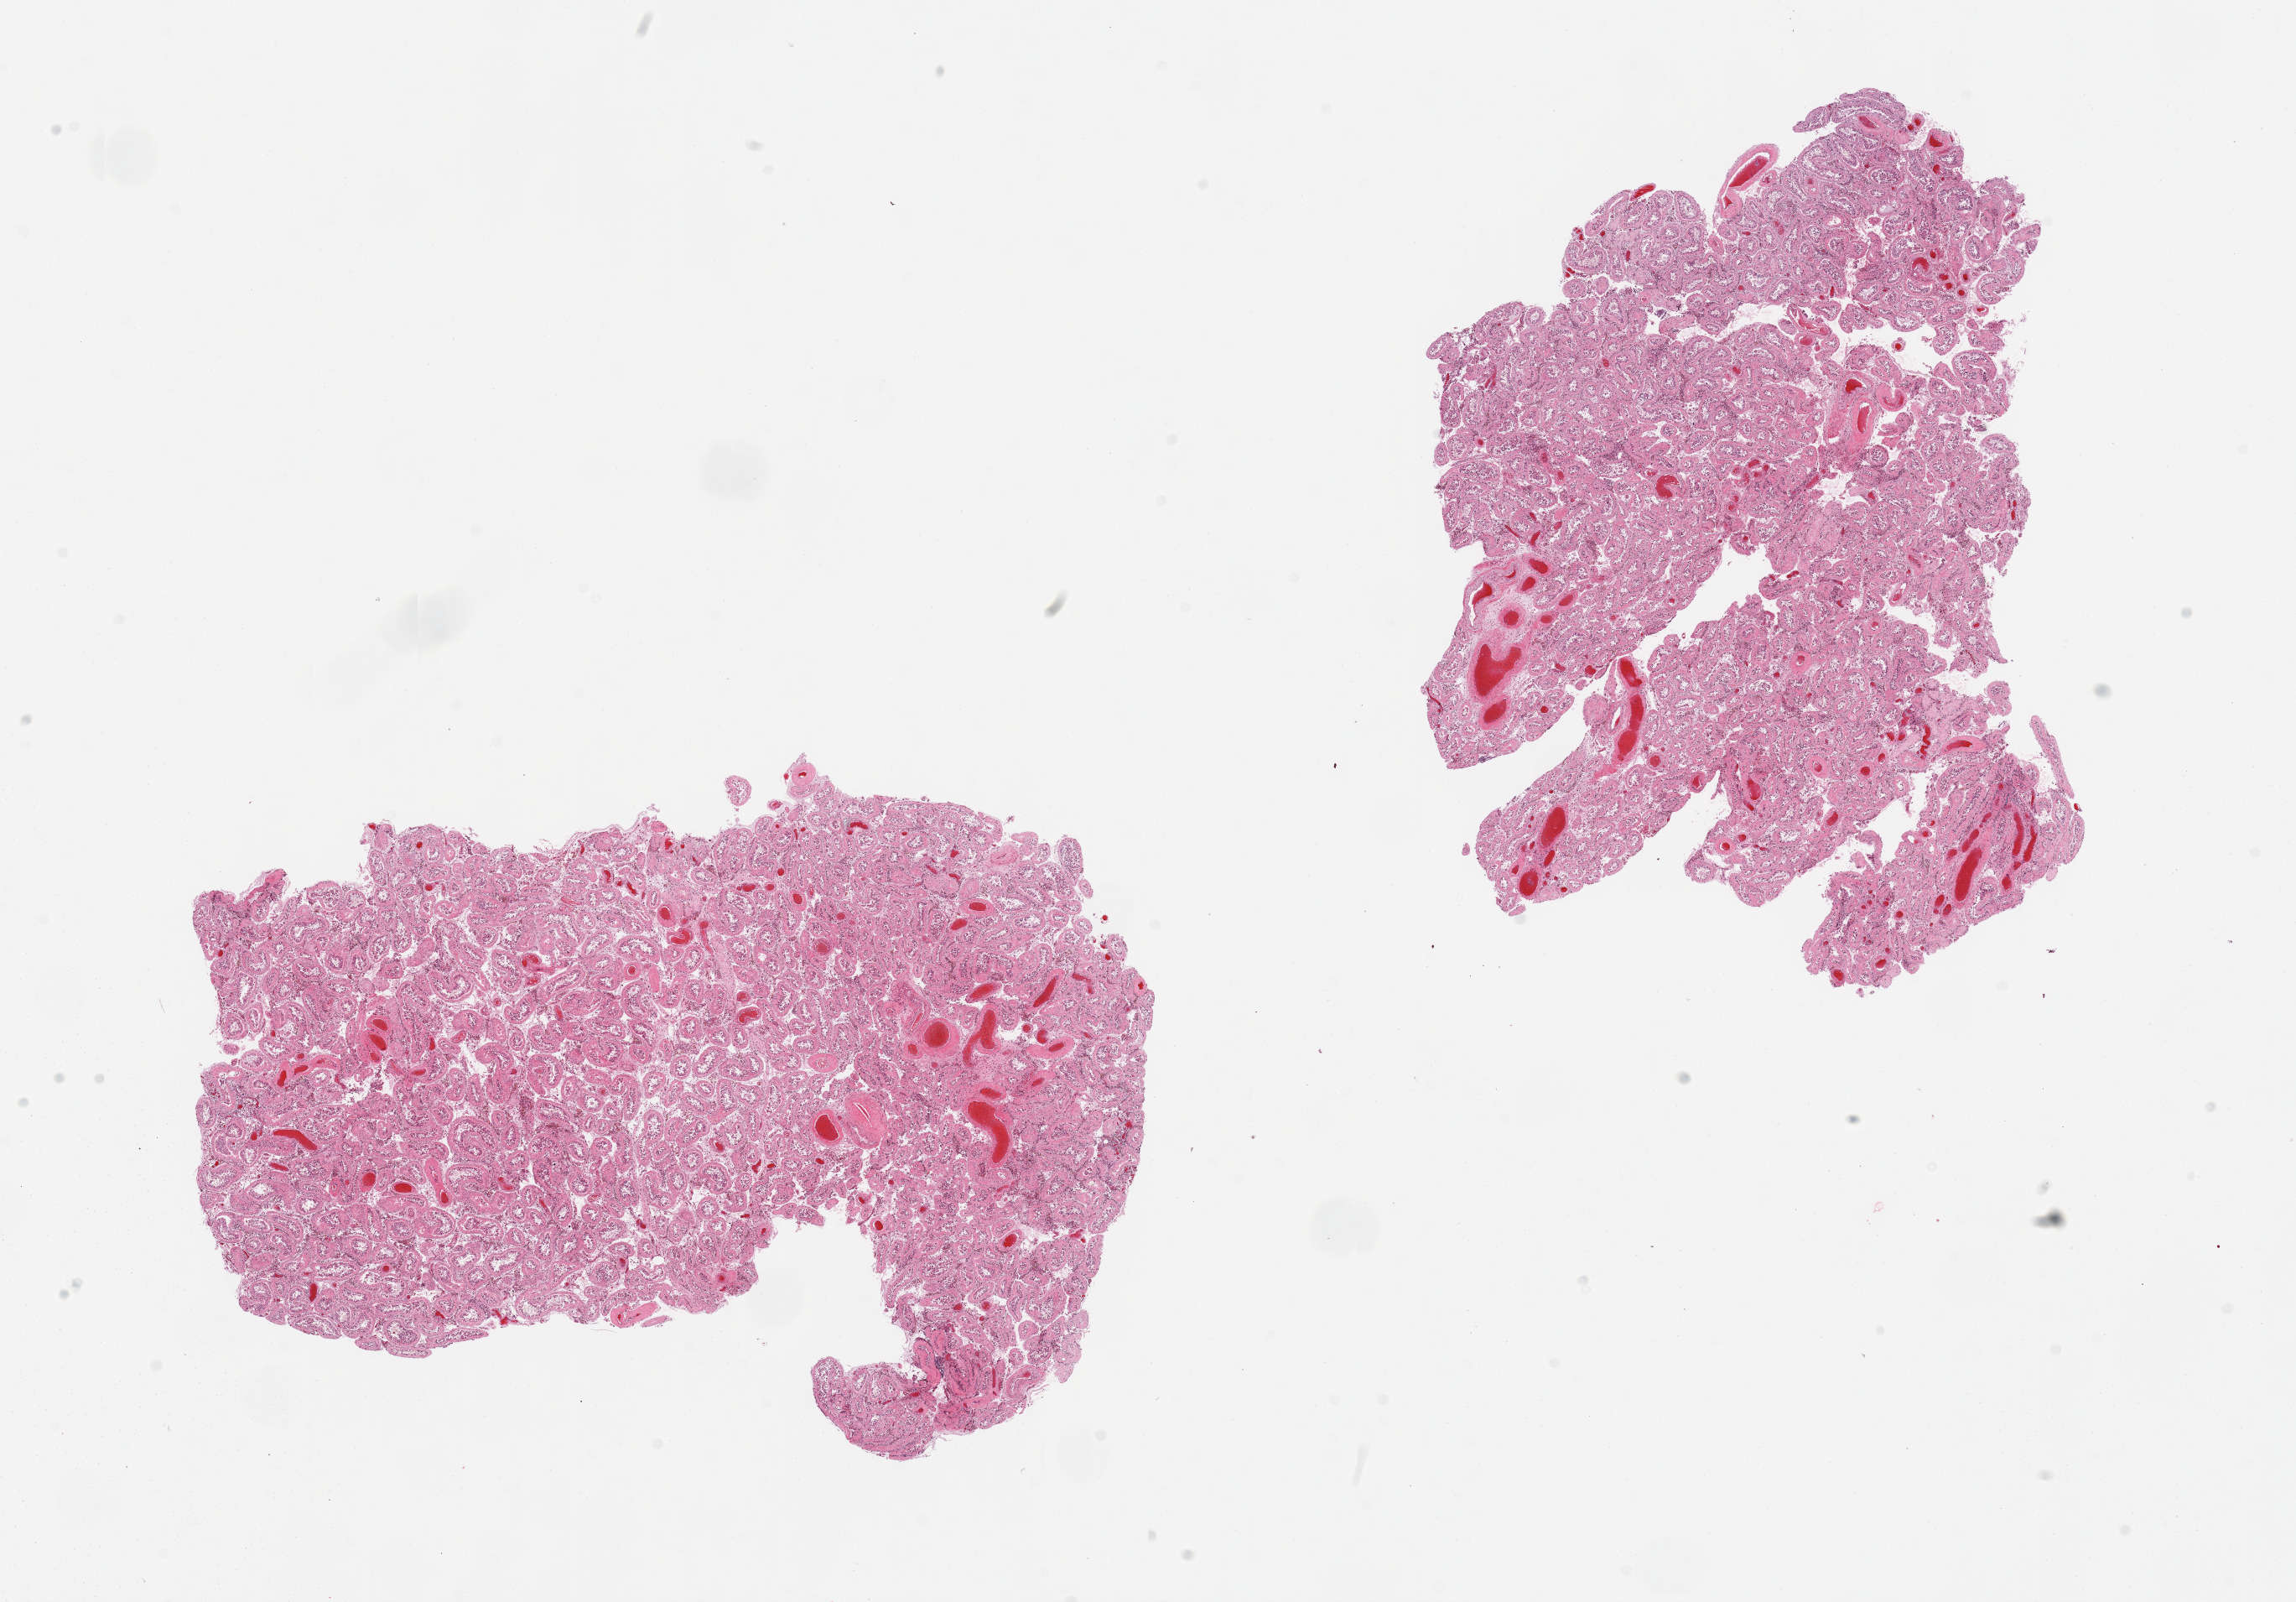
Hematoxylin and eosin (H&E) whole-slide image, low-resolution overview of the scanned area, about 21.7 x 15.1 mm. PAXgene-fixed, paraffin-embedded tissue. Target tissue: testis. Donor tissue sample. Donor: male.
Reviewer comment on this tissue sample: 2 pieces; marked decrease in spermatogenesis; some tubules hyalinized.